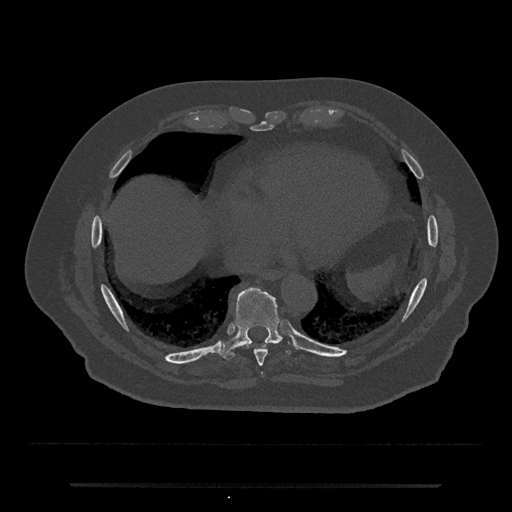
CT including the spine, one axial slice; bone window (W 1800 / L 400 HU); 512 × 512 image matrix, field of view 434 × 434 mm. Male patient, age 80 years. From the clinical record (not read from this slice): primary cancer: prostate; vertebrae with lytic lesions (as recorded): L1, T11.
Outlined on this slice (semi-automatic segmentation, software-assisted and operator-edited):
- T8 vertebra: bounding box [x1, y1, x2, y2] px = [255, 349, 267, 367]
- T9 vertebra: [218, 287, 297, 360]